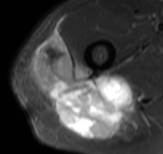
MRI of an extremity soft-tissue mass, one axial slice. STIR. MR volume resampled by the dataset authors to the PET/CT grid (not the native acquisition matrix). 3.27 mm slice thickness. 163 × 154 image matrix, field of view 159 × 150 mm. Male patient. From the clinical record (not read from this slice): histological type: poorly differentiated synovial sarcoma; grade: high; site of the primary tumour: right buttock.
Annotated regions visible in this slice (expert contour drawn on MRI and transferred to this co-registered scan by the dataset authors):
- gross tumour volume including surrounding oedema: bounding box <29,32,145,140> (left, top, right, bottom; pixels)
- gross tumour volume (mass): <29,32,133,140>